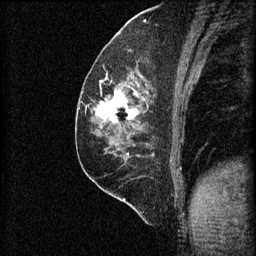
Breast MRI (dynamic contrast-enhanced), one sagittal slice. Slice 32 of 60 in the series (ordered by position). 3 images stored at this slice position (order not interpretable as contrast timing). 1.5 T. TE 4.2 ms, TR 8.2 ms. 2 mm slice thickness. 256 × 256 image matrix, field of view 180 × 180 mm. Female patient, age 59 years.
Annotated regions visible in this slice (semi-automatically segmented with operator editing):
- analysis volume of interest (the breast-tissue region the enhancement analysis was run in; not a lesion): bounding box [x1, y1, x2, y2] px = [92, 74, 154, 131]
- tumour enhancement mask (voxels above the 70 % enhancement threshold inside the analysis volume of interest): [97, 76, 144, 123]